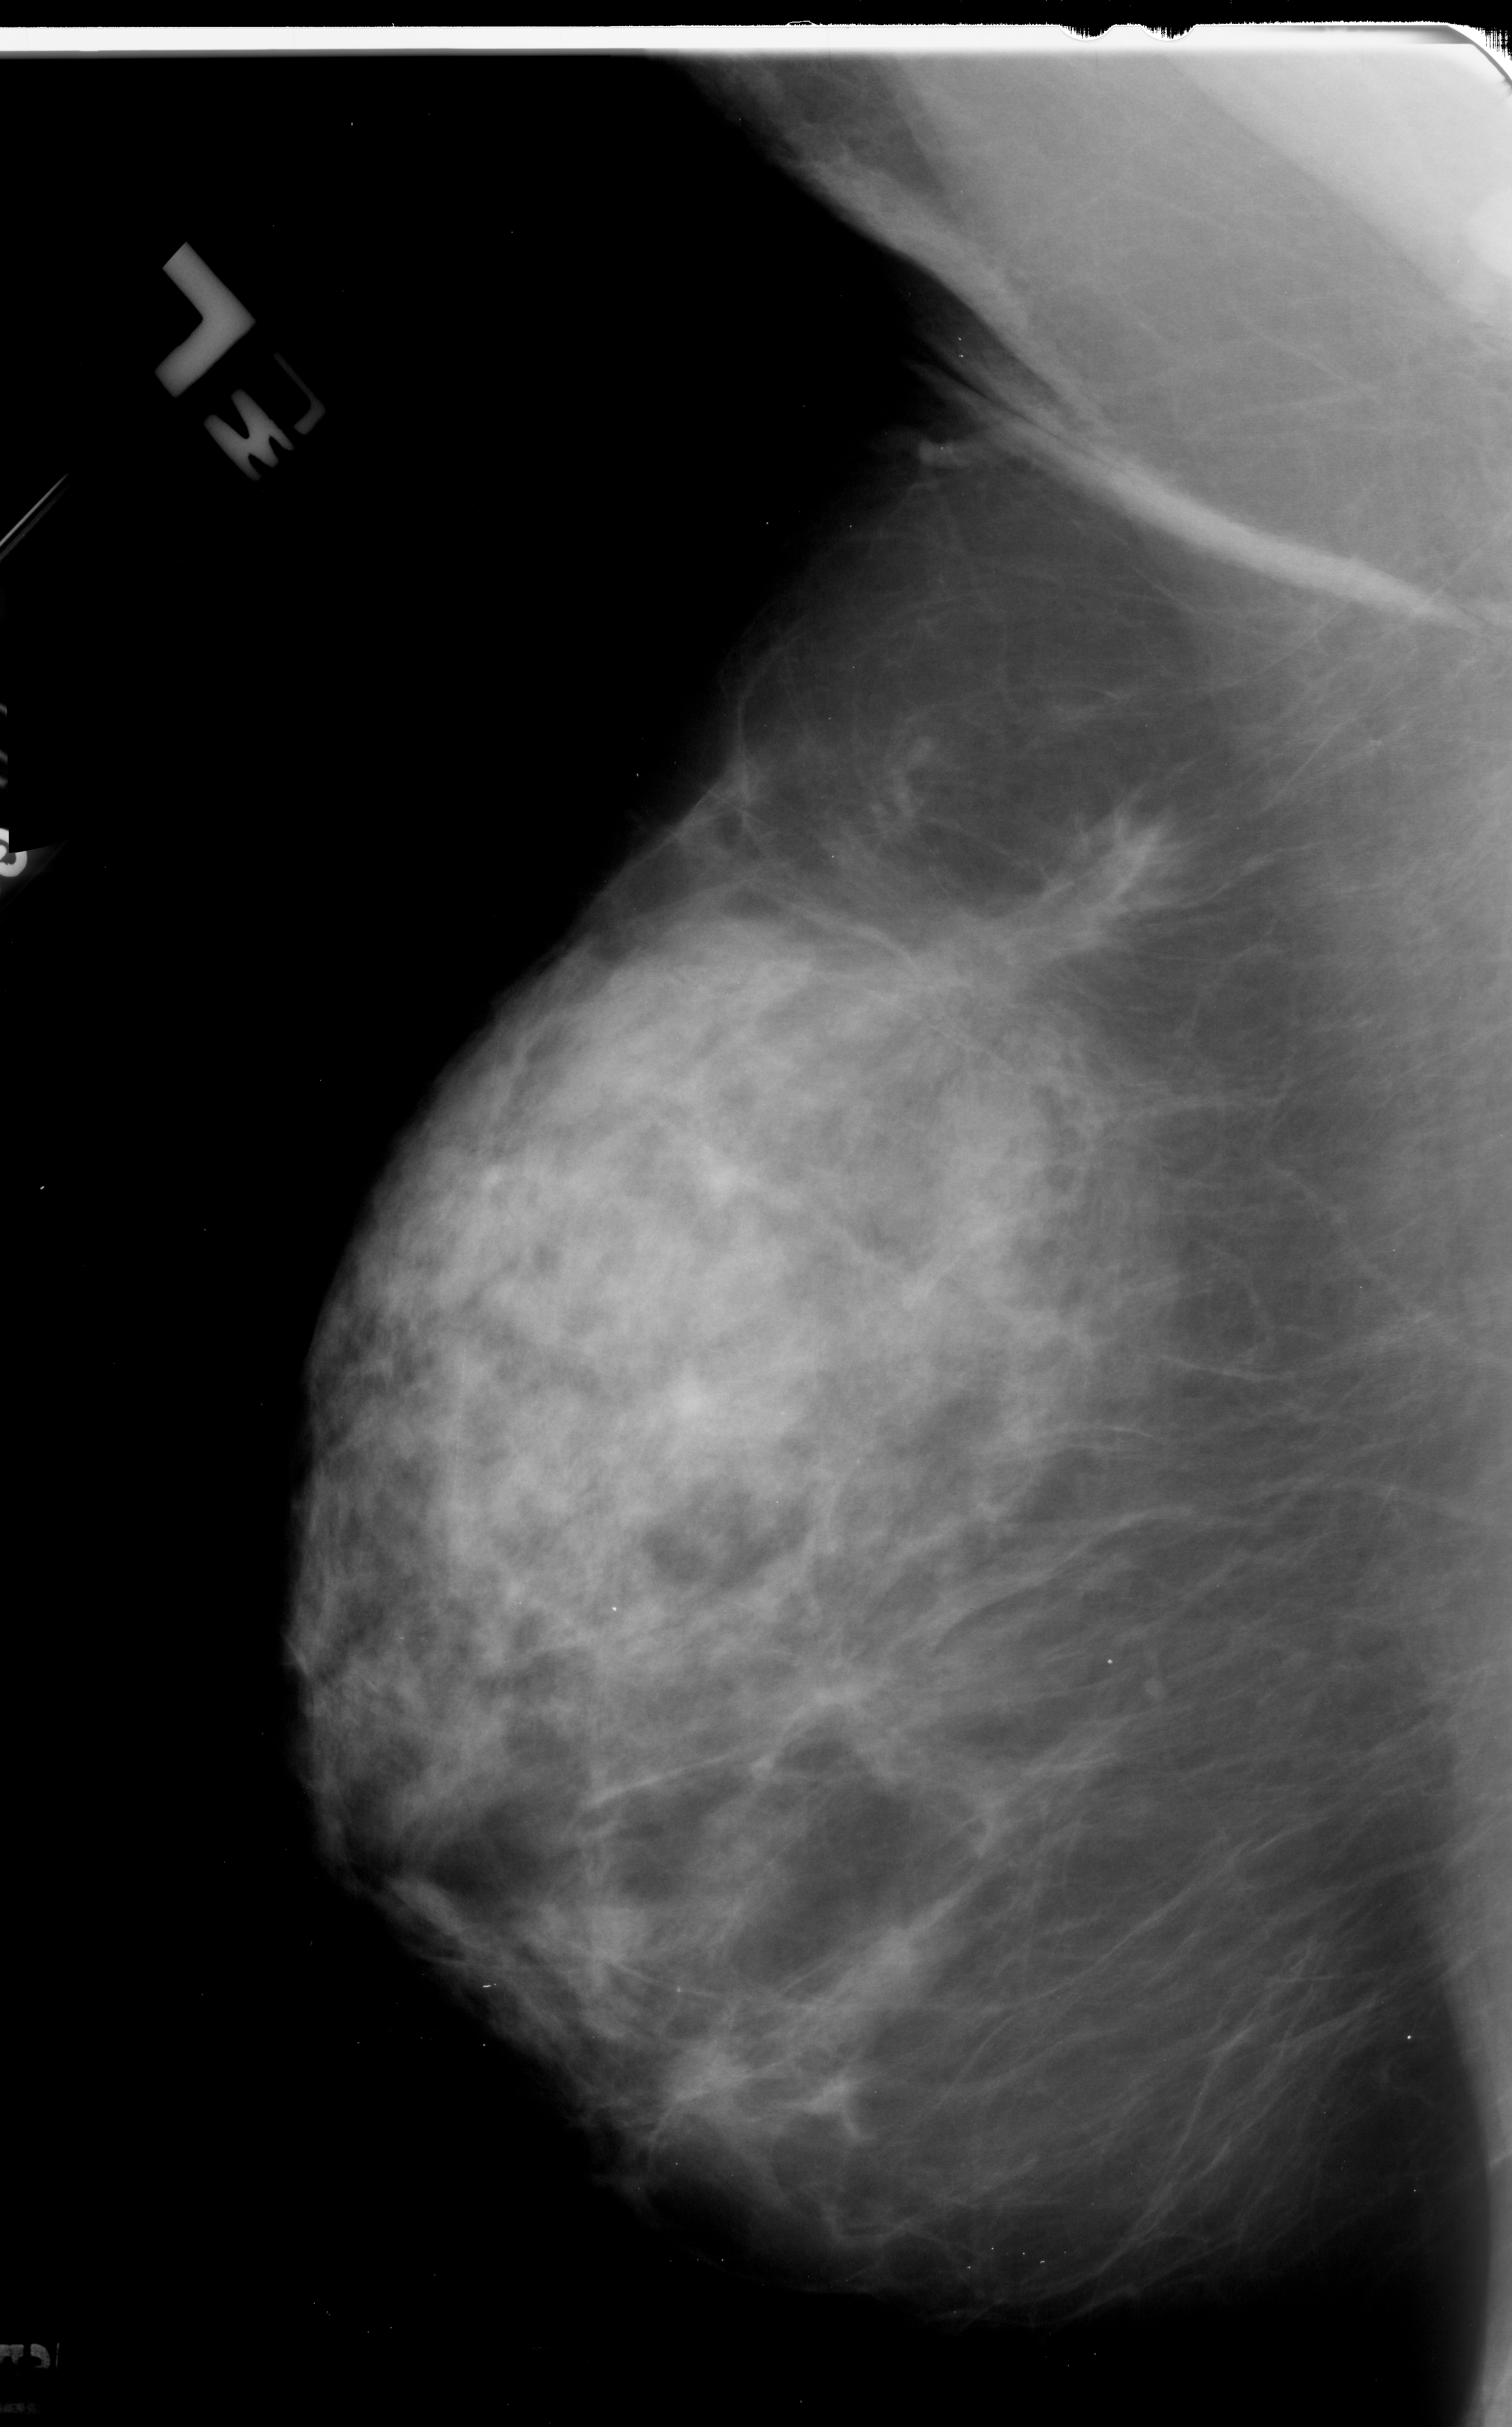
Mammogram (digitized film); left breast; mediolateral oblique (MLO) view; BI-RADS breast density category 3 (scale 1–4); 1512 × 2427 image matrix.
Expert-marked regions of interest on this film, with their recorded descriptors:
- mass, shape architectural distortion, margins spiculated; BI-RADS assessment category 5; subtlety rating 2 on a 1 (subtle) to 5 (obvious) scale; pathology result (as recorded, not read from the image): malignant: bounding box <829,871,1128,1074> (left, top, right, bottom; pixels)